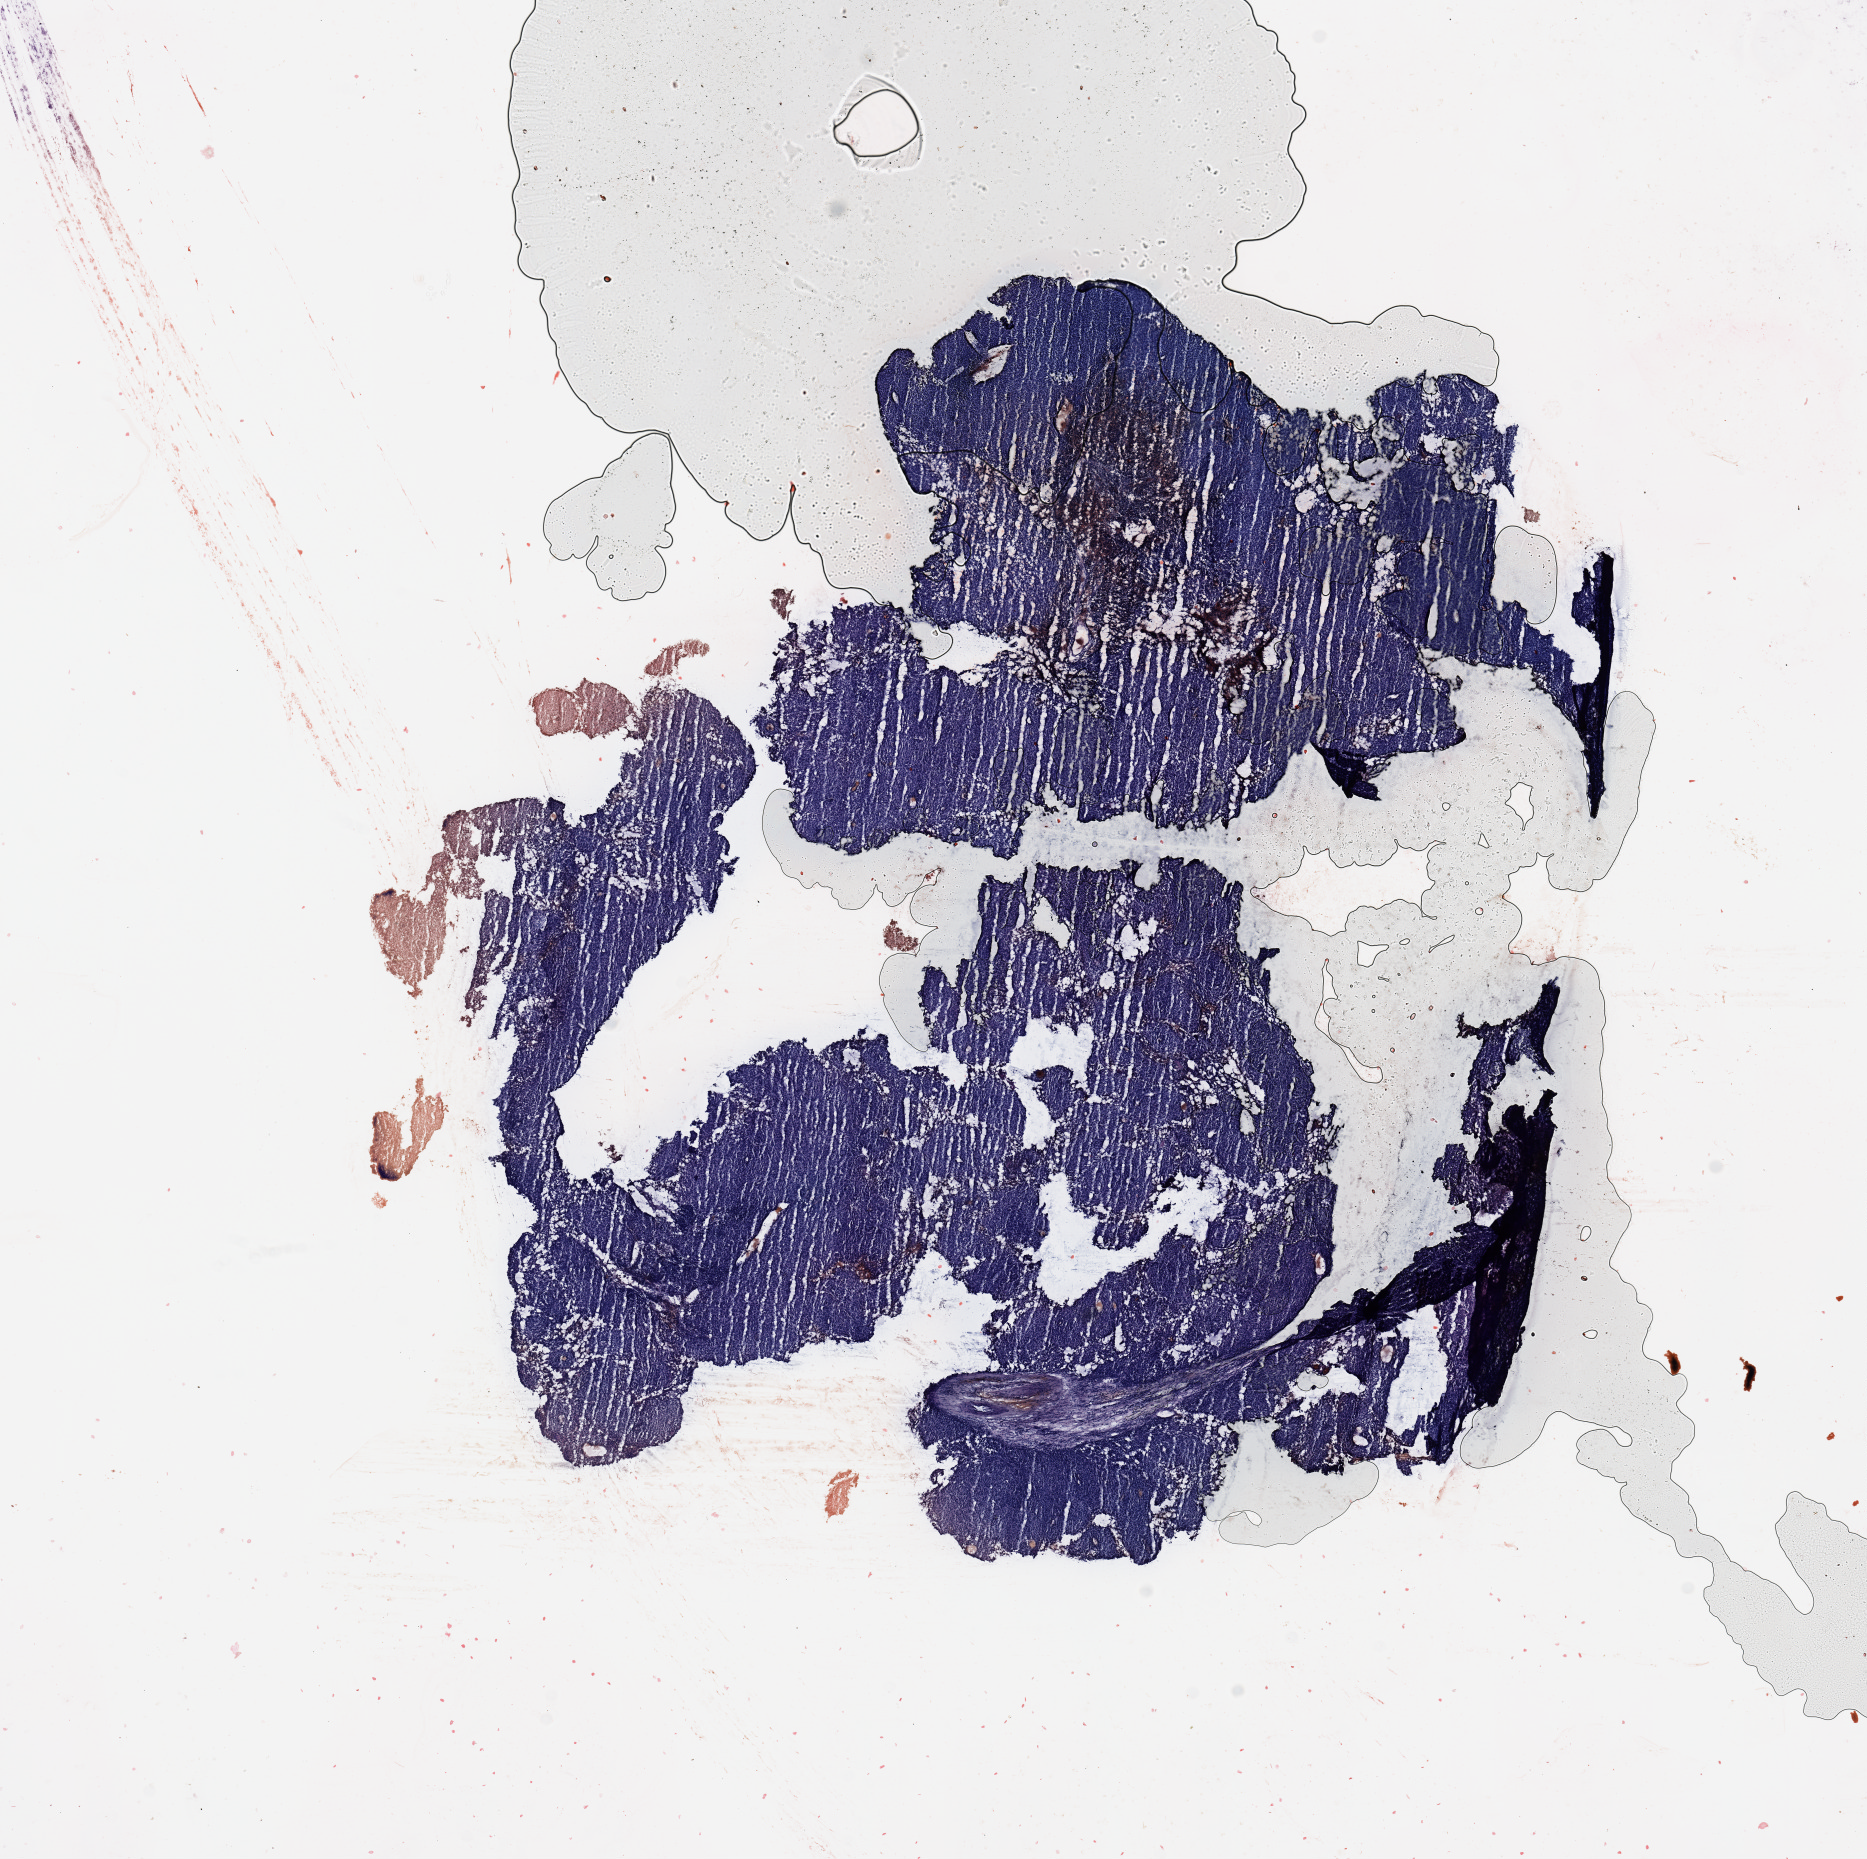
Digitized H&E-stained tissue section (whole slide), whole scanned area (about 14.8 x 14.7 mm) shown as a low-resolution overview, melanoma tumour tissue; sampled site not recorded. Male, 66 y/o.
Patient diagnosis (cohort enrolment): cutaneous melanoma (skin).